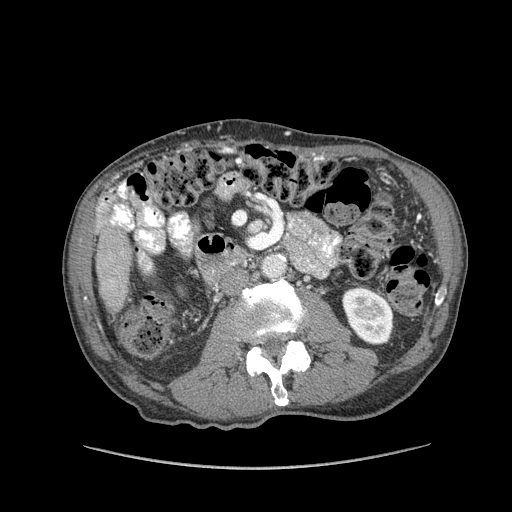
Contrast-enhanced abdominal CT (liver protocol), one axial slice; slice 15 of 162 in the series (ordered by position); 100 kVp; soft-tissue window (W 400 / L 40 HU); 2.5 mm slice thickness; 512 × 512 image matrix, field of view 400 × 400 mm. From the clinical record (not read from this slice): diagnosis: hepatocellular carcinoma (patient treated with transarterial chemoembolisation; whether this scan precedes or follows treatment is not stated here); TNM stage (as recorded): Stage-IIIA; Child-Pugh class: A; tumour nodularity: multinodular.
Annotated regions visible in this slice (semi-automatically segmented with operator editing):
- liver parenchyma outside the tumour (the mass and vessels are separate outlines, so this box may not span the whole liver): bounding box (x1, y1, x2, y2) in pixels: (96, 195, 132, 314)
- liver vessels: (99, 203, 117, 225)